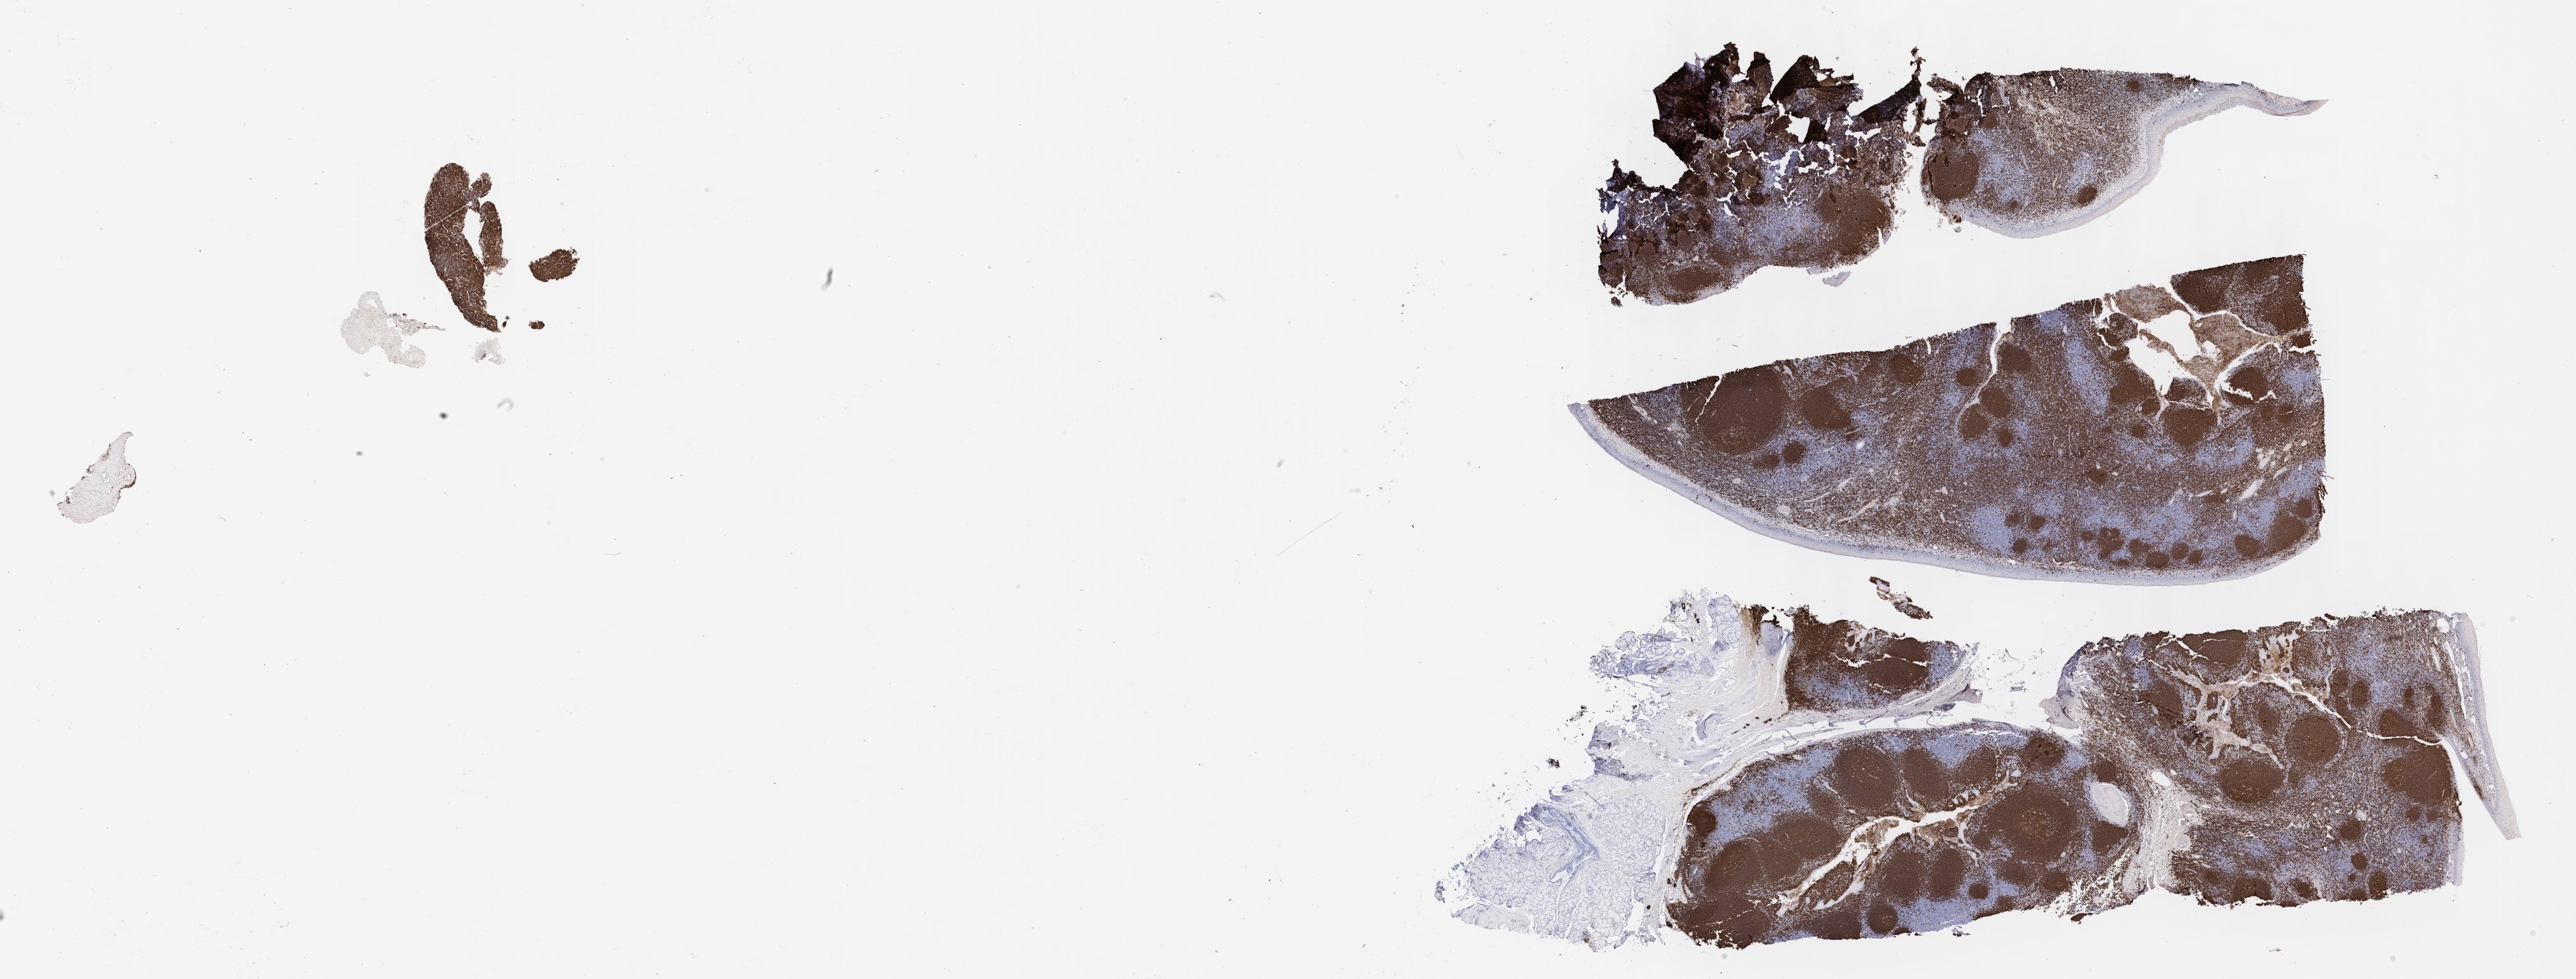
Whole-slide image, immunohistochemical stain for CD20, a low-resolution overview of the entire scanned area, about 32.7 x 12.4 mm. Tumor tissue. Site: abdomen proper. Patient: female, age at initial diagnosis 7 years.
Histologic diagnosis: Burkitt lymphoma, NOS.